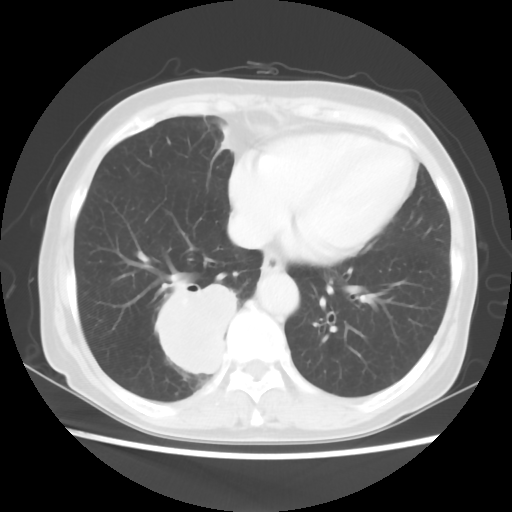
Chest CT, one axial slice. Position 18 of 56 along the scan axis. 120 kVp. Lung window (W 1500 / L -600 HU). 512 × 512 image matrix, field of view 332 × 332 mm. Female patient, age 66 years. From the clinical record (not read from this slice): clinical TNM (as recorded): T2 N3 M0; histopathological grade: G3.
Outlined on this slice (bounding box drawn by a radiologist):
- lung tumour (recorded histology: small cell carcinoma): bounding box (x1, y1, x2, y2) in pixels: (155, 272, 245, 386)